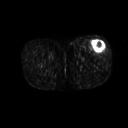
FDG PET of an extremity soft-tissue mass (from a PET/CT study), one axial slice; position 226 of 267 along the scan axis; 3.27 mm slice thickness; 128 × 128 image matrix. Patient: male, 64 years. Case-level facts recorded for this patient, not image findings: histological type: extraskeletal osteosarcoma; grade: high; site of the primary tumour: thigh.
Structures marked on this image (expert contour drawn on MRI and transferred to this co-registered scan by the dataset authors):
- gross tumour volume (mass): box from (x=91, y=41) to (x=106, y=52) px